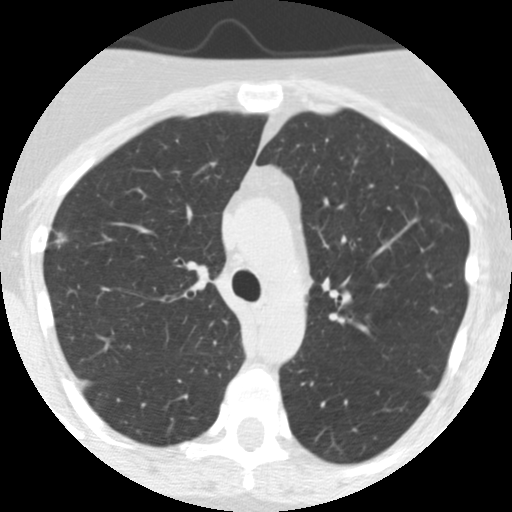
Low-dose screening chest CT, axial slice. Baseline annual screen. Lung window (W 1500 / L -600 HU). 512 × 512 image matrix. Female participant, aged 55 years at enrolment. Current smoker at enrolment.
• Lesion marked by an expert reader, bounding box (x1, y1, x2, y2) in pixels: (29, 218, 83, 265).
• The exam's reader record, not a measurement of the box and not confirmed to be the same lesion: non-calcified nodule or mass ≥4 mm, right upper lobe, 7 × 7 mm, spiculated (stellate) margins, soft tissue attenuation.
• Official screen result: positive, change unspecified: nodule(s) >= 4 mm or enlarging nodule(s), mass(es), or other non-specific abnormalities suspicious for lung cancer.
• Lung cancer was diagnosed 1018 days after this screen (after the third annual screen): bronchiolo-alveolar adenocarcinoma, NOS, right upper lobe, moderately differentiated (G2), stage IIA (AJCC 6th edition), 13 mm at pathology.